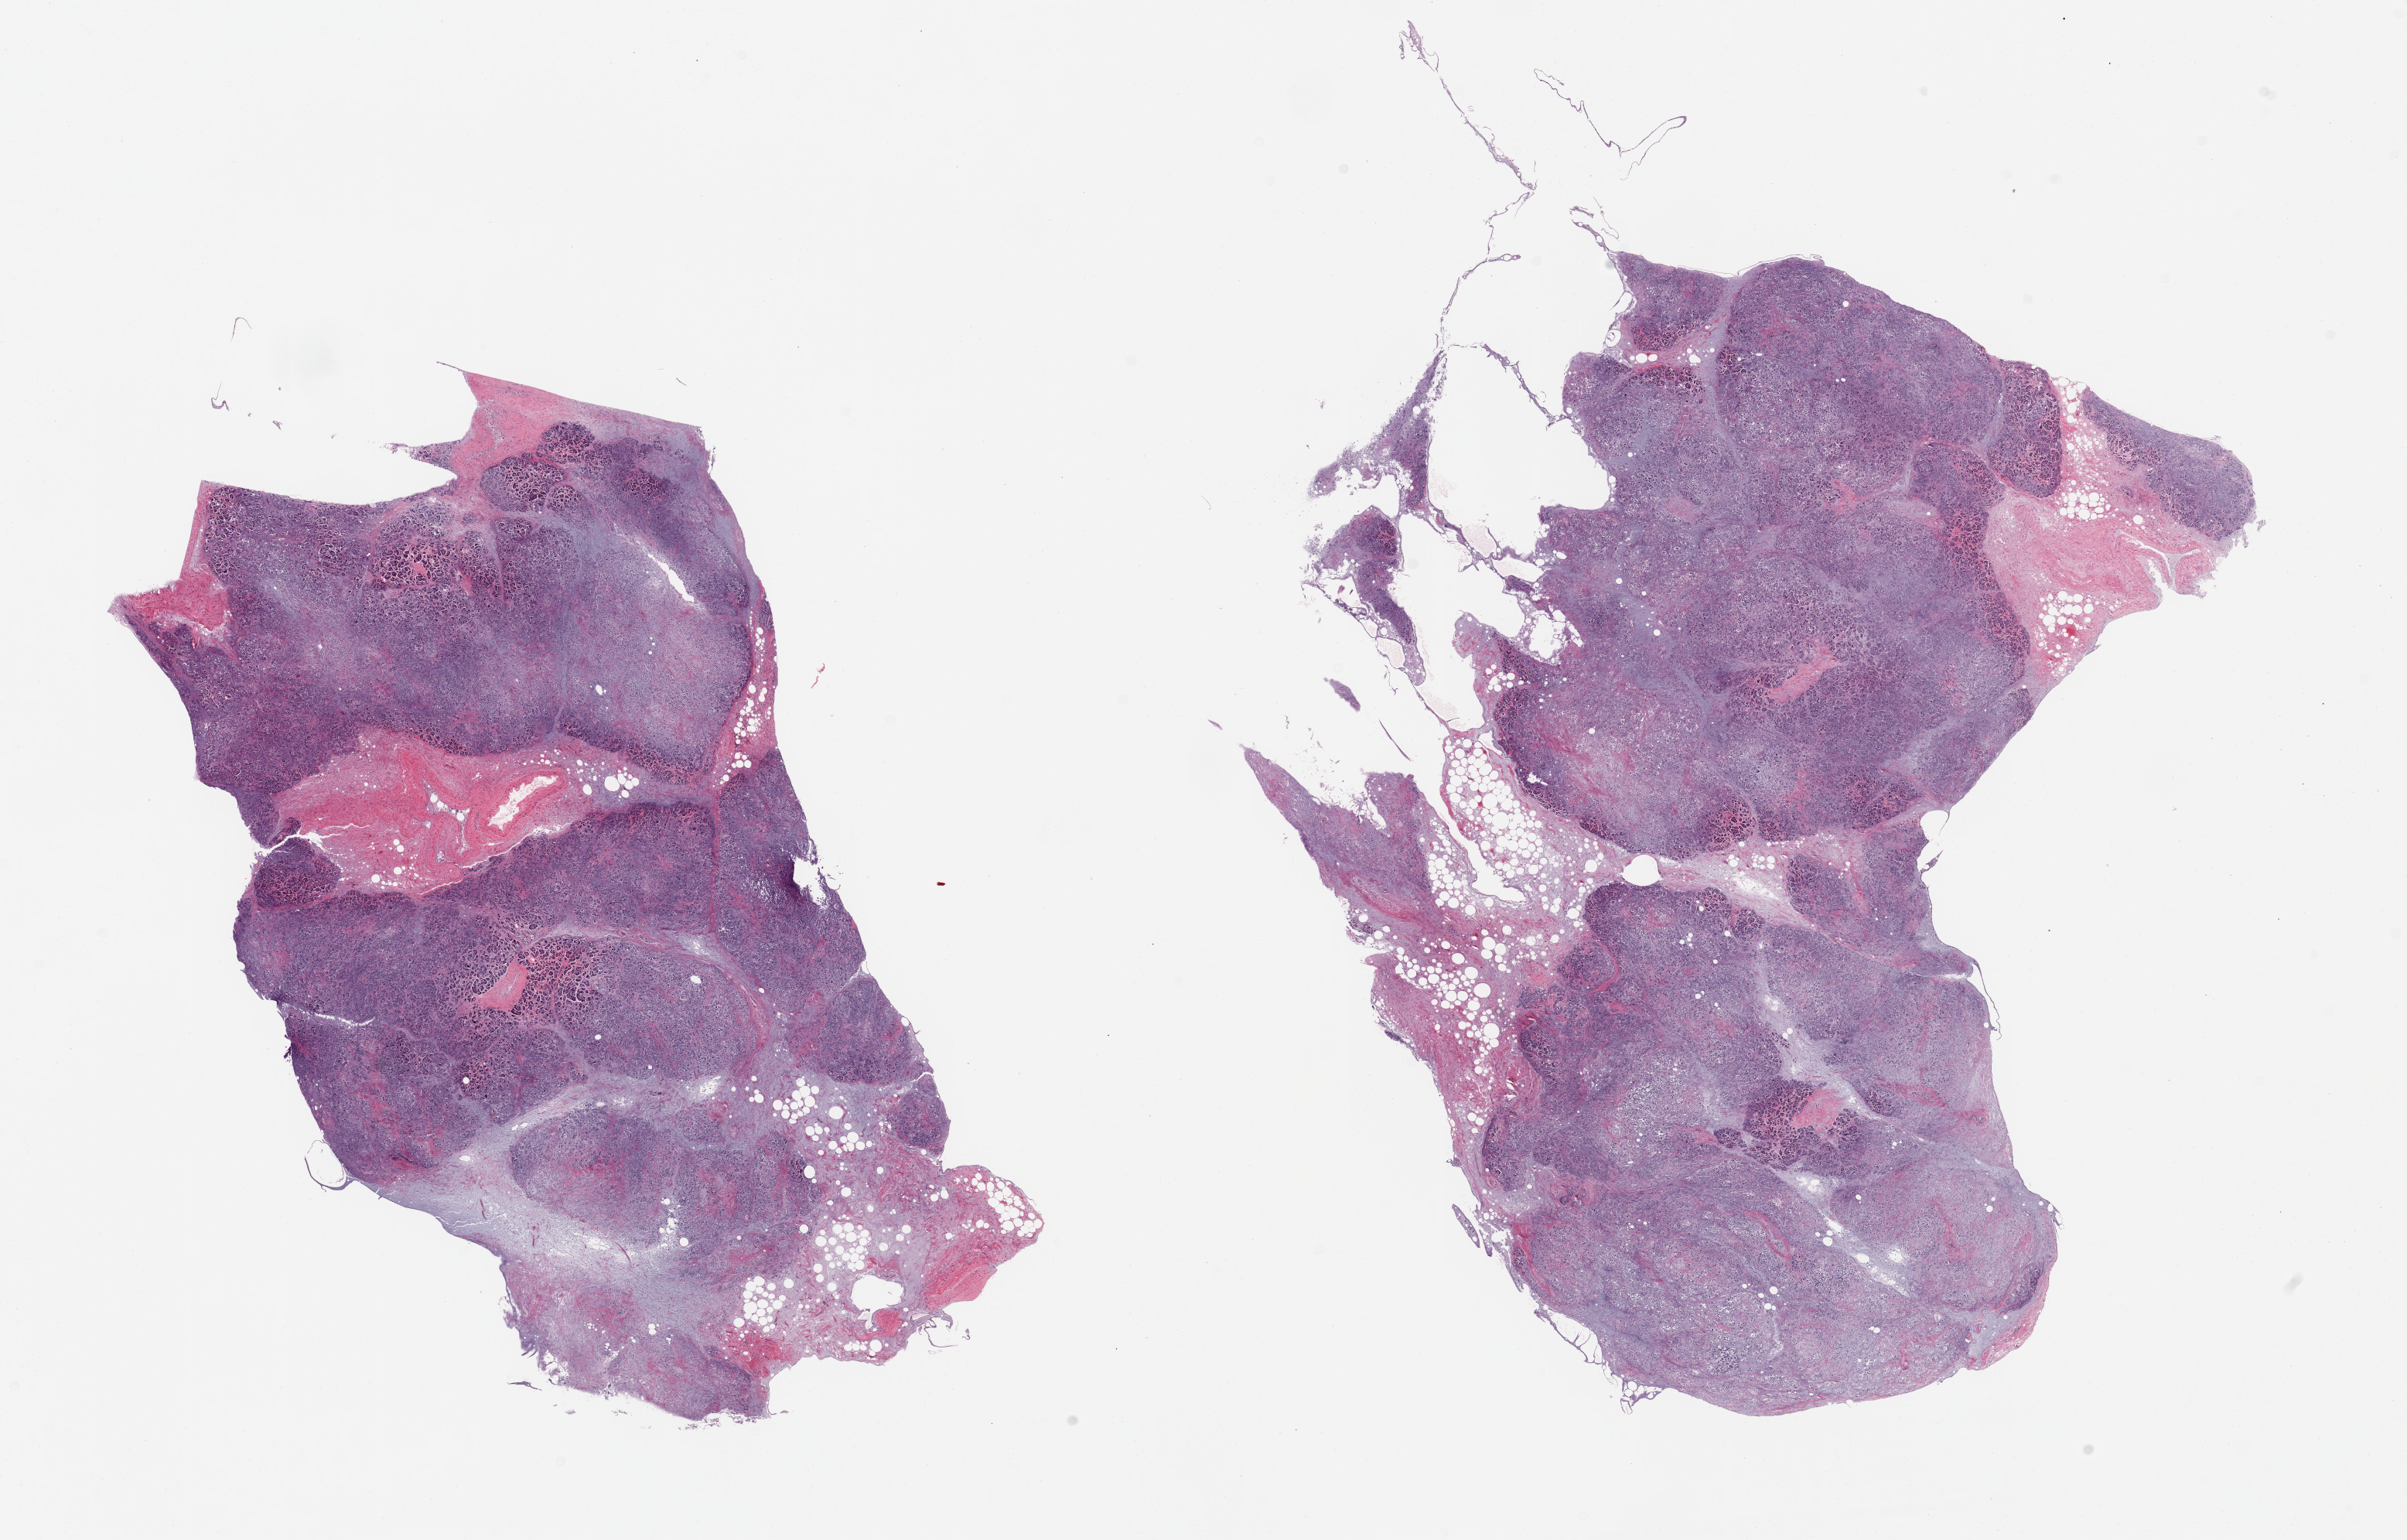
Whole-slide image, hematoxylin and eosin (H&E) stain, low-resolution overview of the scanned area, about 24.6 x 15.7 mm (from a 20x scan); PAXgene-fixed, paraffin-embedded tissue; sampled site (target tissue): pancreas; tissue donor sample. Donor: female.
- pathologist's review note for this sample: 2 pieces; severely autolyzed